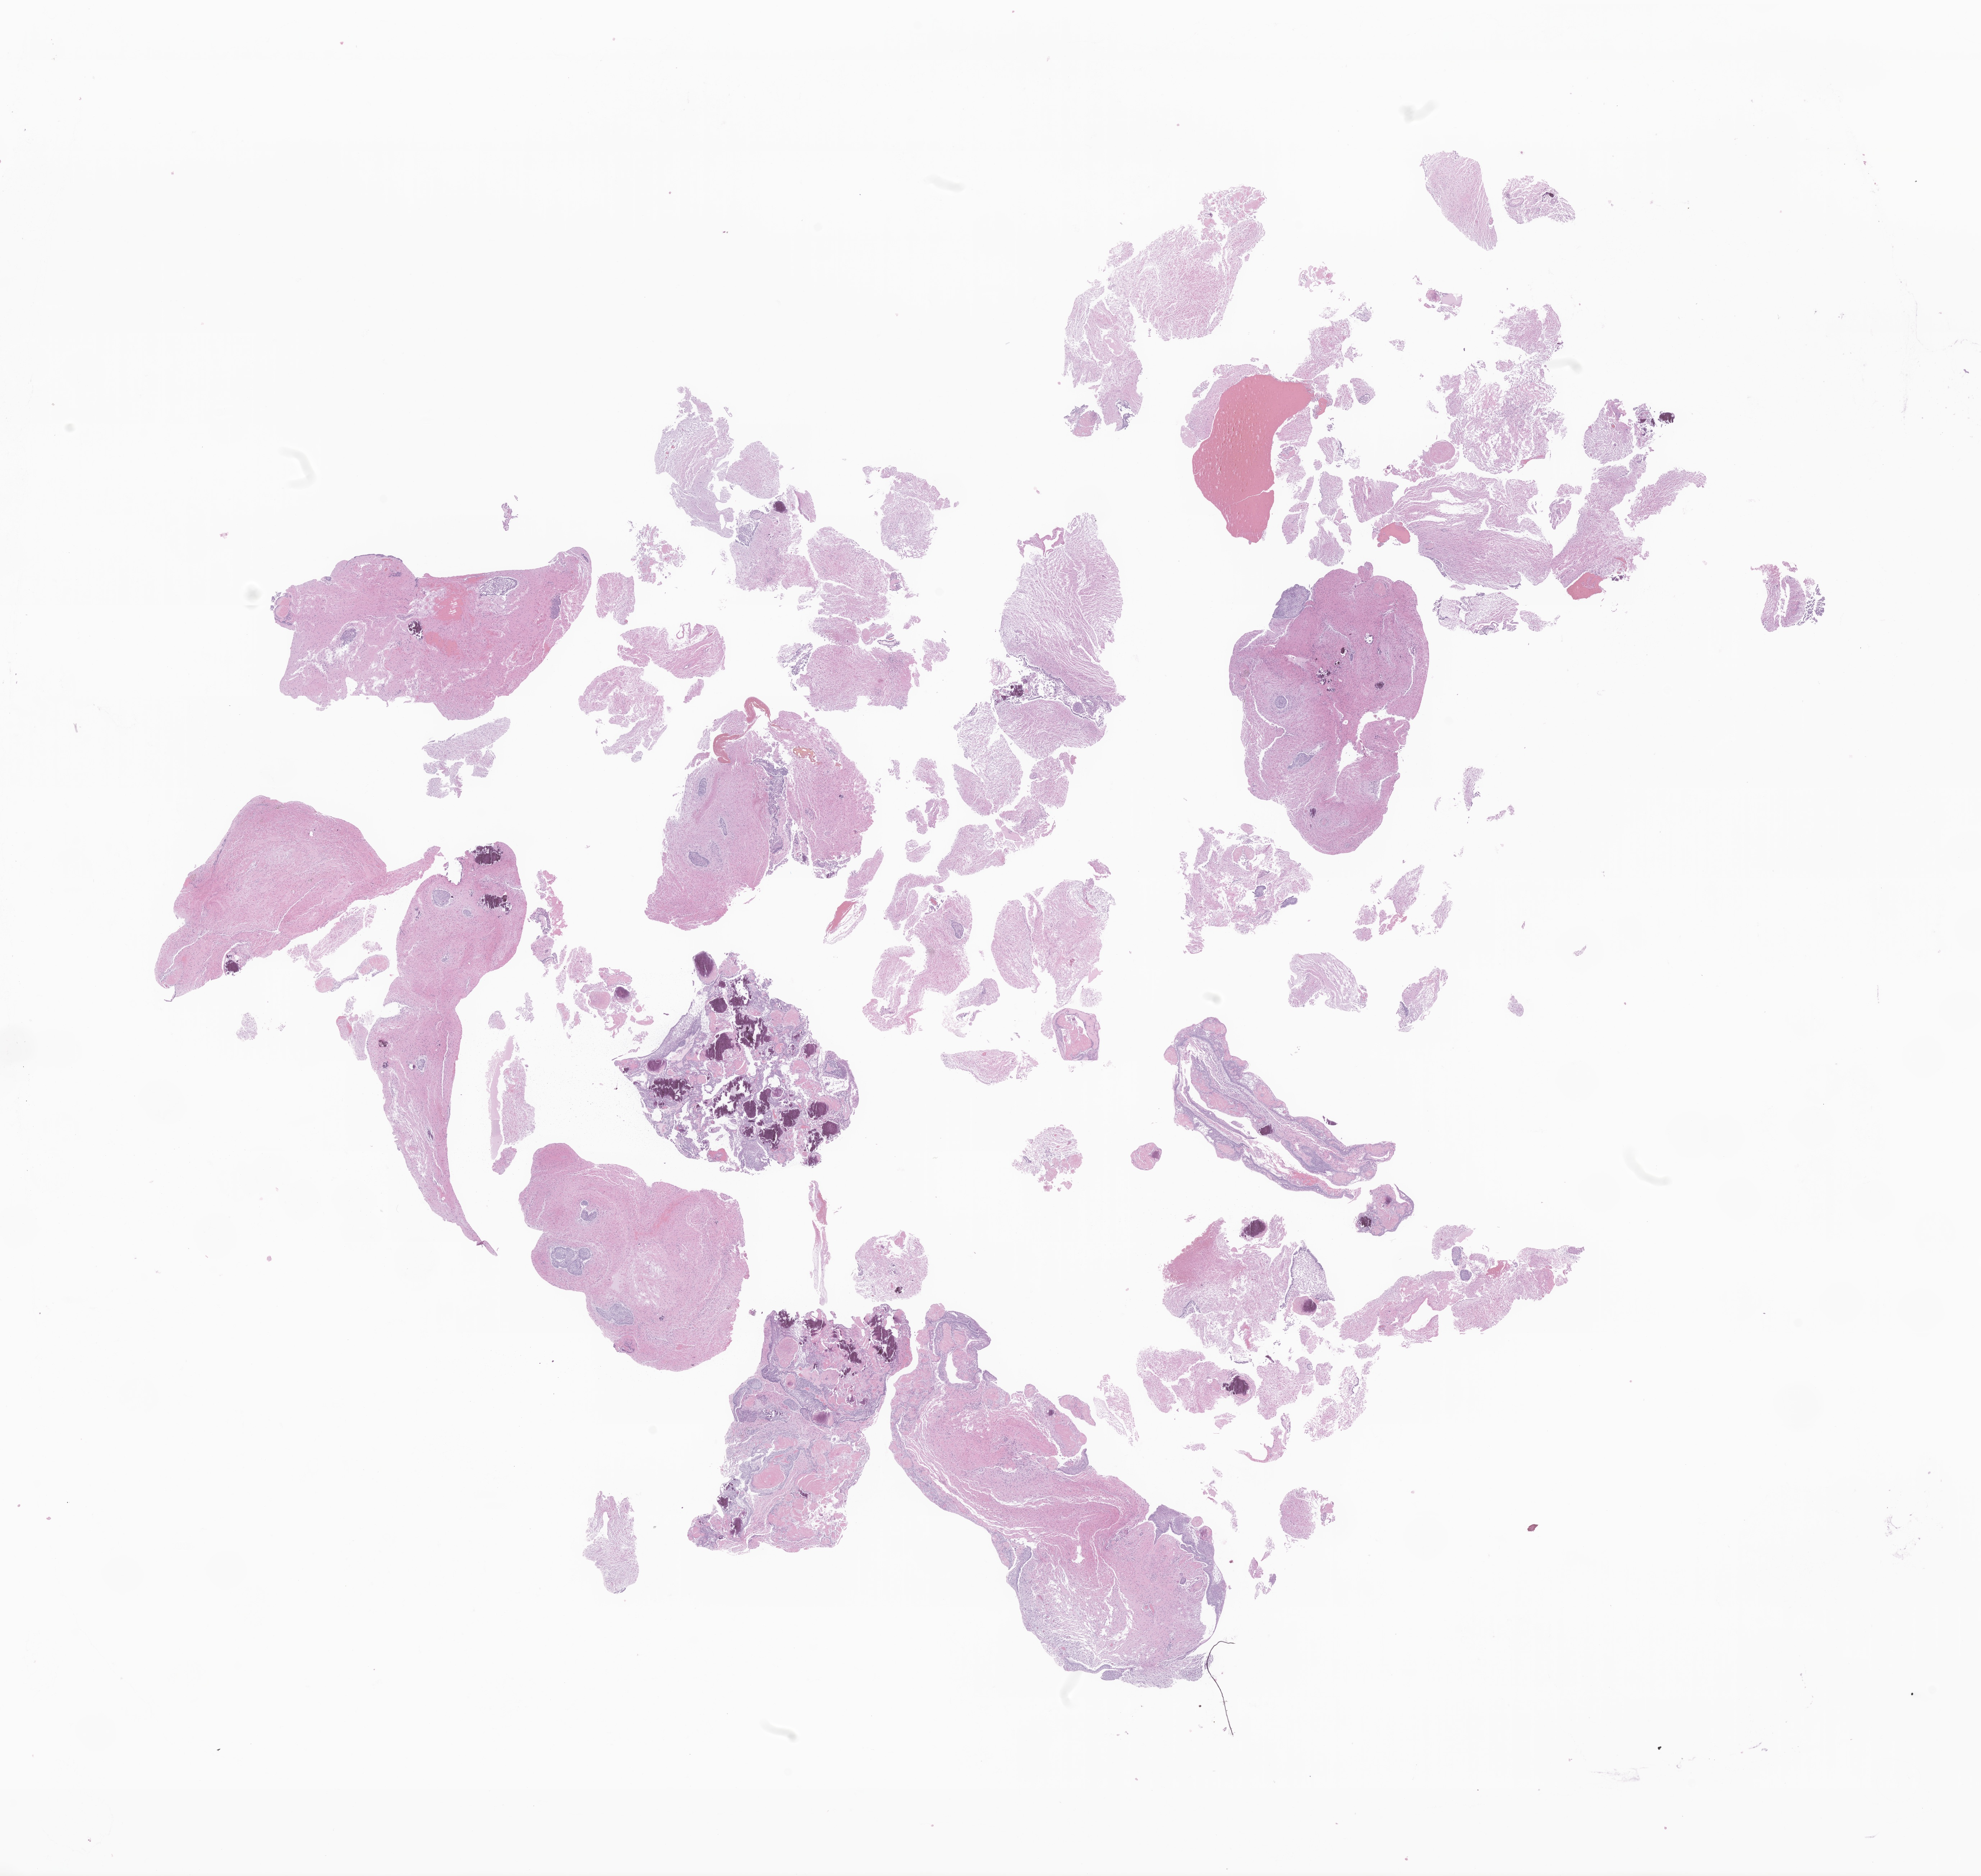
Whole-slide image, haematoxylin and eosin stain of tumor tissue from the brain — low-resolution overview of the scanned area, about 23.2 x 22.0 mm. Formalin-fixed paraffin-embedded section. Patient male; age 164 months (13 years 8 months).
Diagnosis: Craniopharyngioma, NOS.